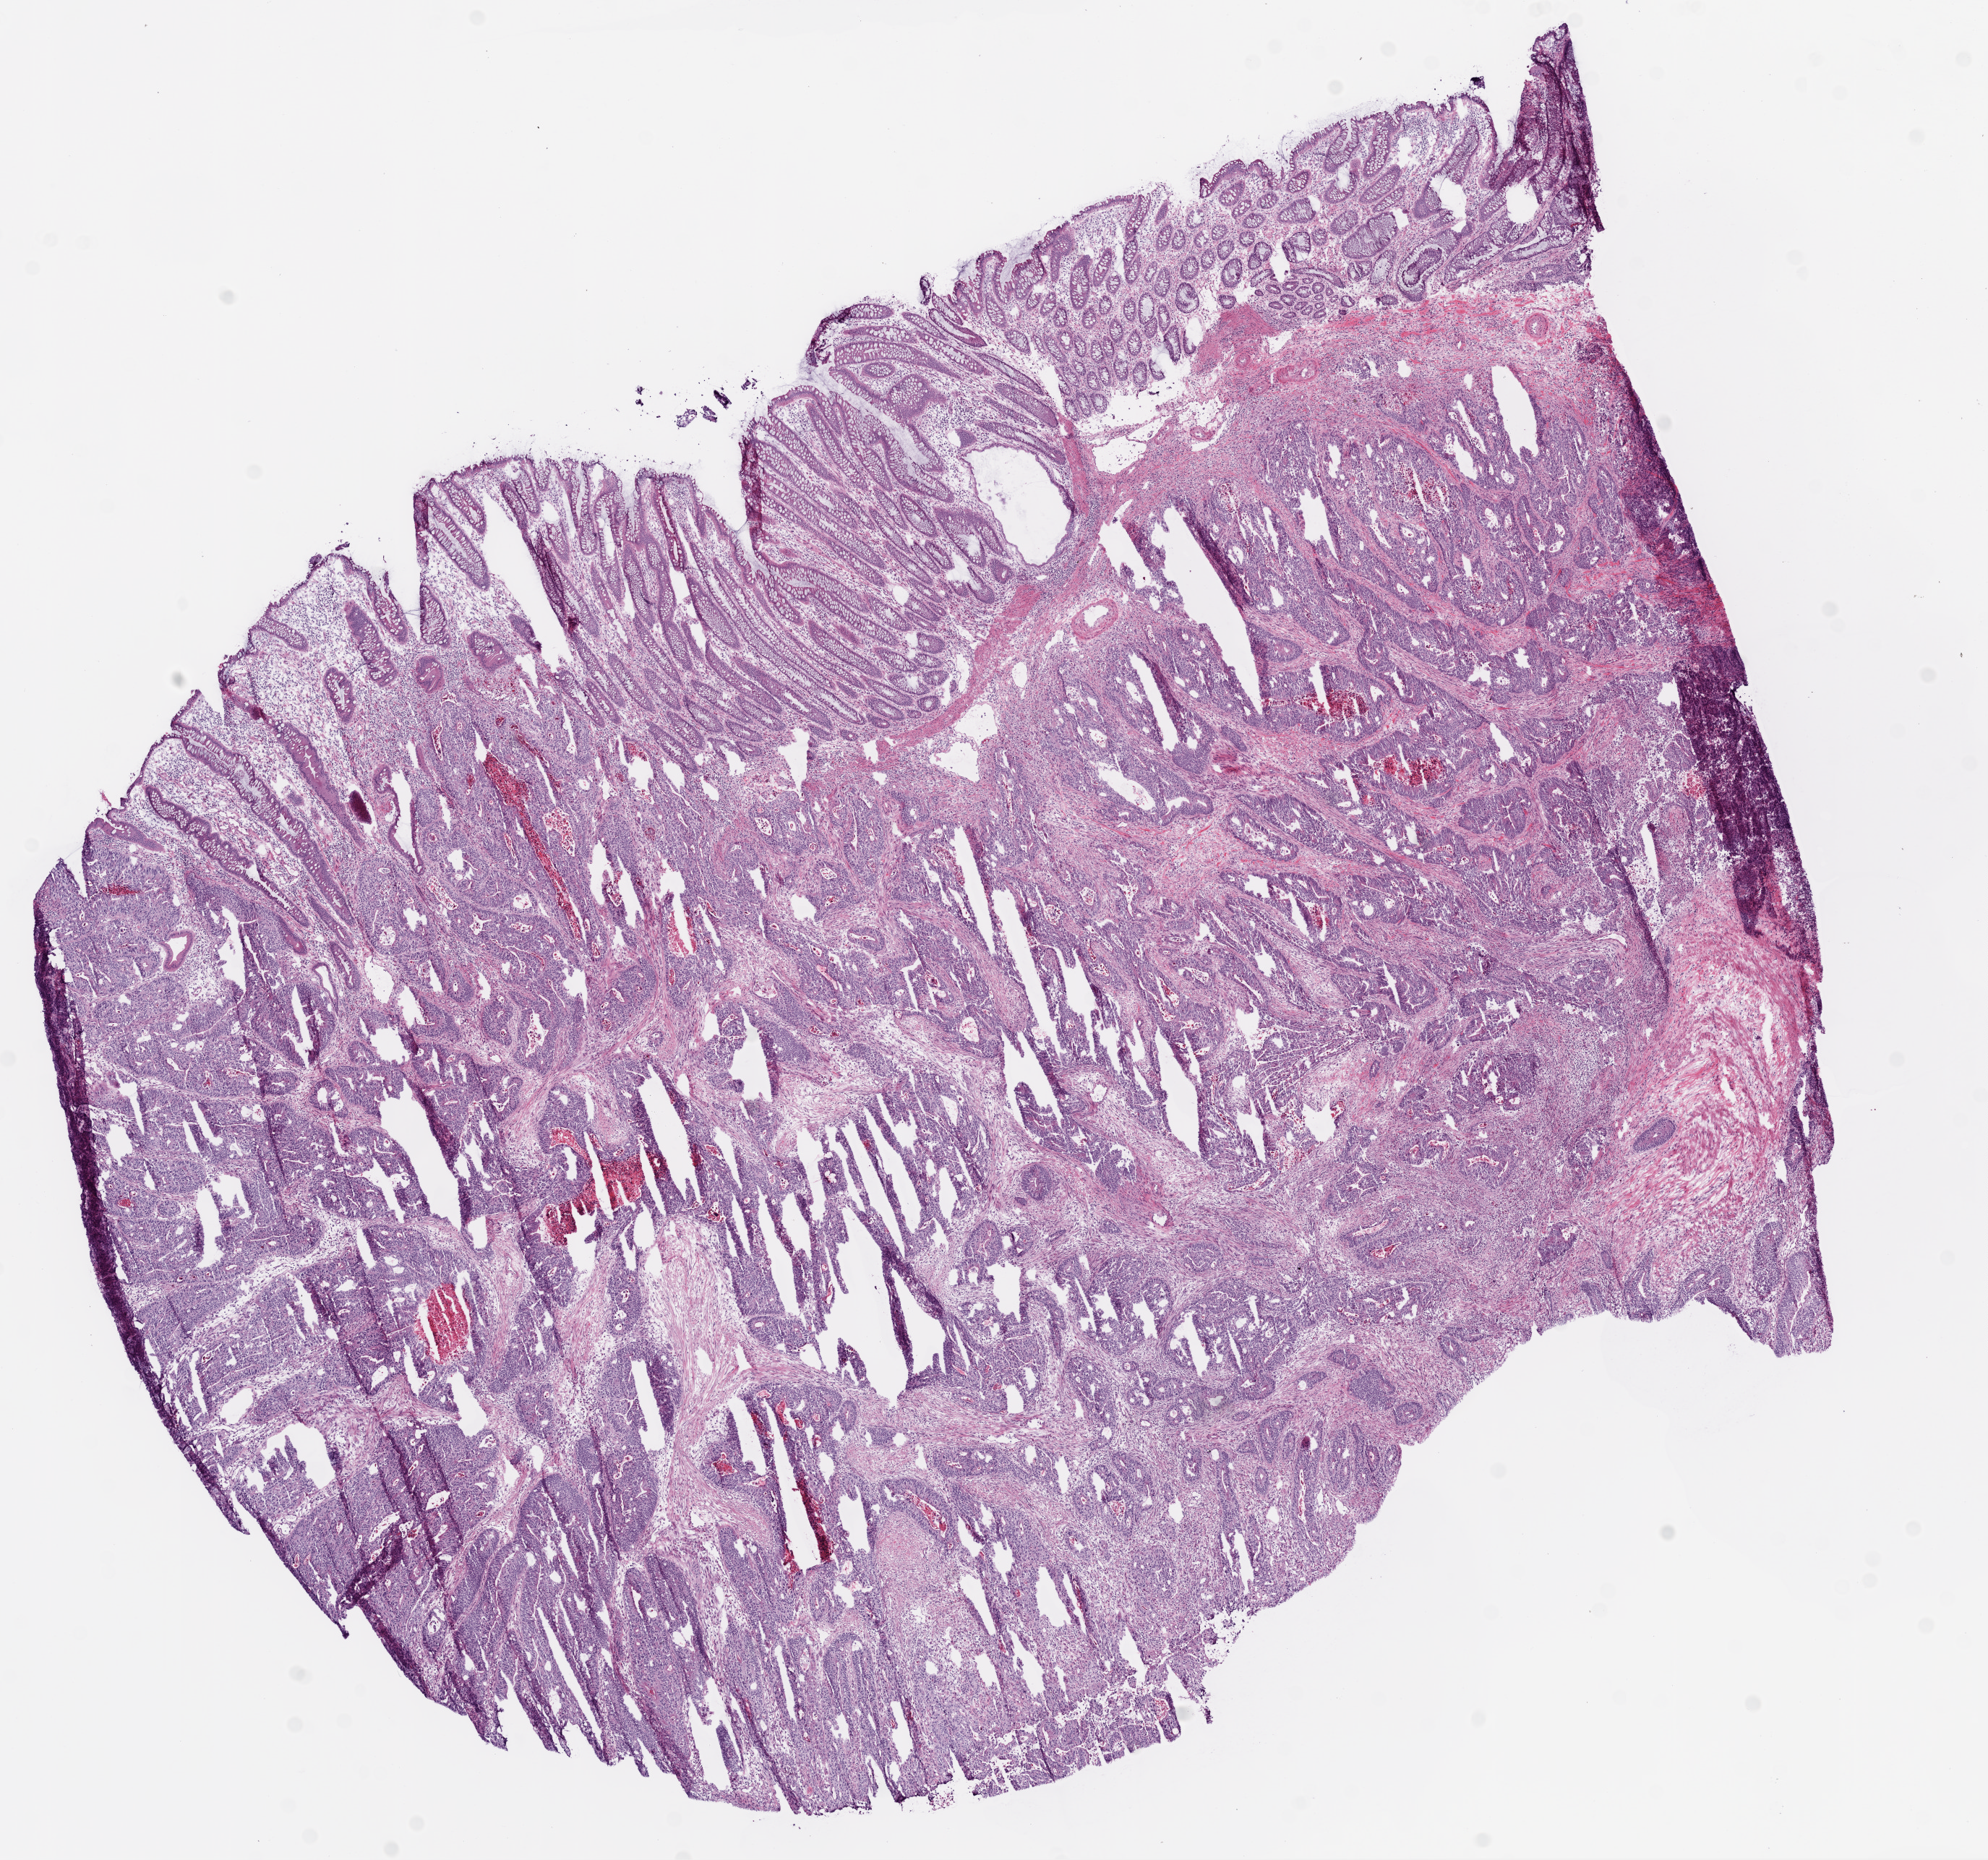
Whole-slide histology image, Hematoxylin and eosin (H&E) stained — low-resolution overview of the scanned area, about 11.0 x 10.3 mm (from a 20x scan). Frozen section from the bottom of the tissue portion. Primary tumour sample from the colon. Patient: female, age at initial diagnosis 72 years. Composition of this section per pathologist review: tumour cells 72%, tumour nuclei 70%, normal cells 10%, stromal cells 15%, necrosis 7%.
Lymph nodes positive (case pathology): 0 of 34 examined. Histologic diagnosis: Adenocarcinoma, NOS (hepatic flexure of colon). TNM: T3 N0 M0. AJCC pathologic stage: II (6th edition).